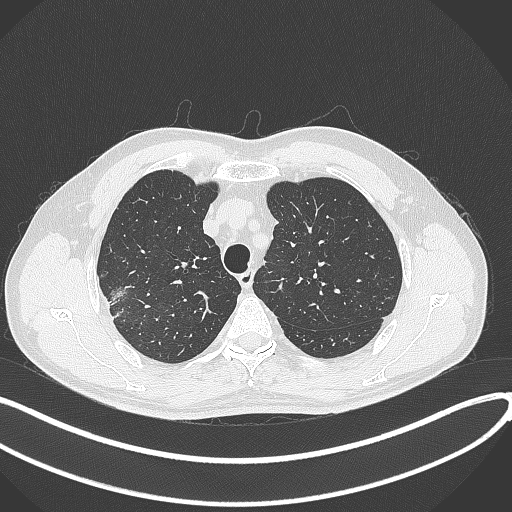
Chest CT, one axial slice; position 334 of 381 along the scan axis; lung window (W 1500 / L -600 HU); 1 mm slice thickness; 512 × 512 image matrix, field of view 400 × 400 mm. Male patient, age 62 years. Case-level facts recorded for this patient, not image findings: clinical TNM (as recorded): T1c N0 M0; histopathological grade: G2-3.
Structures marked on this image (bounding box drawn by a radiologist):
- lung tumour (recorded histology: adenocarcinoma): bounding box [x1, y1, x2, y2] px = [108, 283, 130, 320]